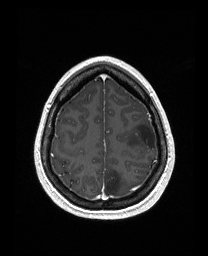
Brain MRI from a brain-tumour surgery series, one axial slice; position 128 of 176 along the scan axis; T1-weighted post-contrast; 1 mm slice thickness; 208 × 256 image matrix, field of view 203 × 250 mm. From the clinical record (not read from this slice): histopathology: Astrocytoma; WHO grade: 3; IDH mutation: yes; tumour location: Left Frontal.
Structures marked on this image (manually delineated by an expert):
- tumour: bounding box <126,121,157,150> (left, top, right, bottom; pixels)